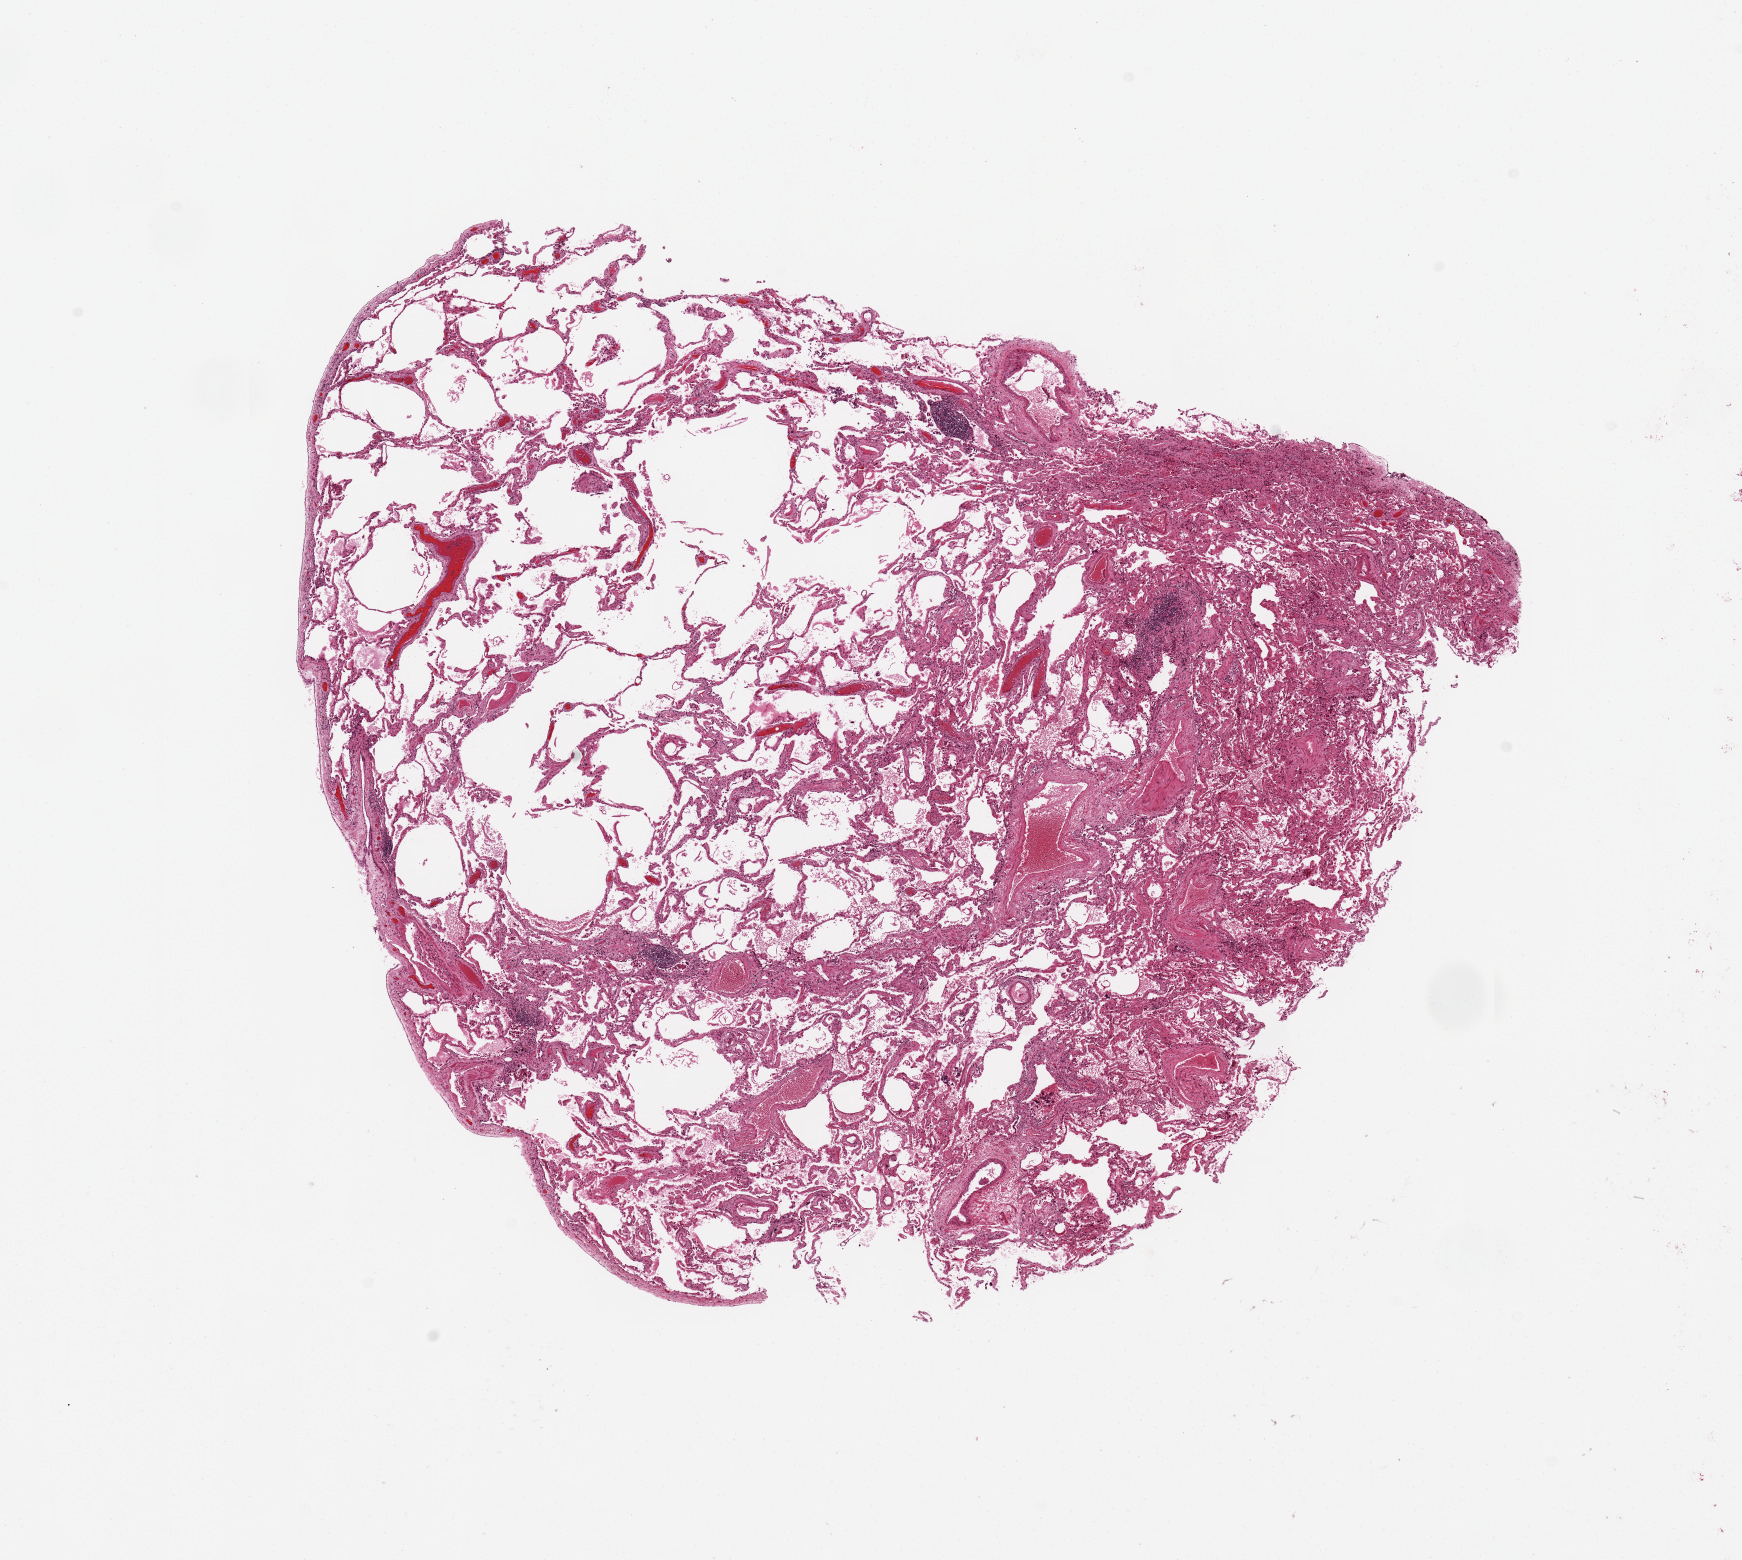
Digitized H&E-stained section, a low-resolution overview of the entire scanned area, about 13.8 x 12.3 mm; PAXgene-fixed, paraffin-embedded tissue; sampled site (target tissue): lung; tissue donor sample. Female donor.
Reviewer comment on this tissue sample: 9x8mm. Emphysema???moderate/severe. Foci of chronic interstitial inflammation, non-specific.